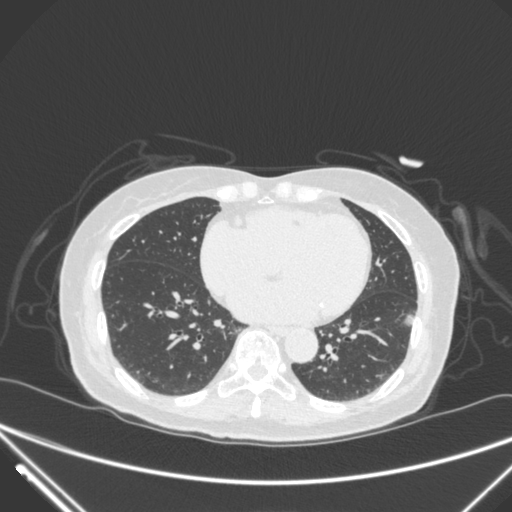
Chest CT, one axial slice; position 118 of 310 along the scan axis; 120 kVp; lung window (W 1500 / L -600 HU); 1 mm slice thickness; 512 × 512 image matrix, field of view 377 × 377 mm. Female patient, age 82 years. From the clinical record (not read from this slice): clinical TNM (as recorded): T1c N0 M0.
Outlined on this slice (bounding box drawn by a radiologist):
- lung tumour (recorded histology: adenocarcinoma): bounding box <393,304,414,331> (left, top, right, bottom; pixels)